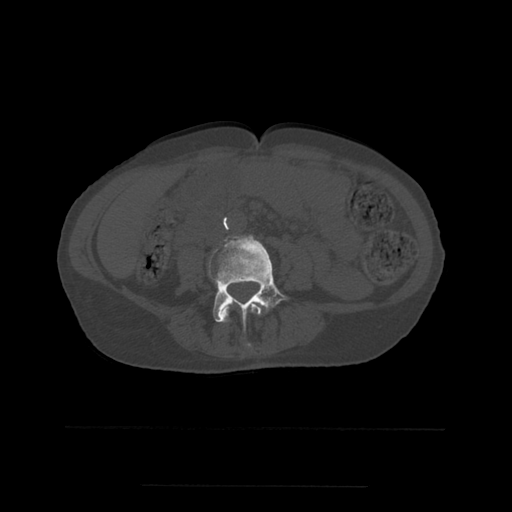
CT including the spine, one axial slice. Position 172 of 544 along the scan axis. Bone window (W 1800 / L 400 HU). 1.25 mm slice thickness. 512 × 512 image matrix, field of view 350 × 350 mm. Patient age 58 years. Case-level facts recorded for this patient, not image findings: primary cancer: lung.
Outlined on this slice (semi-automatic segmentation, software-assisted and operator-edited):
- L3 vertebra: bounding box <220,302,262,347> (left, top, right, bottom; pixels)
- L4 vertebra: <209,235,288,330>